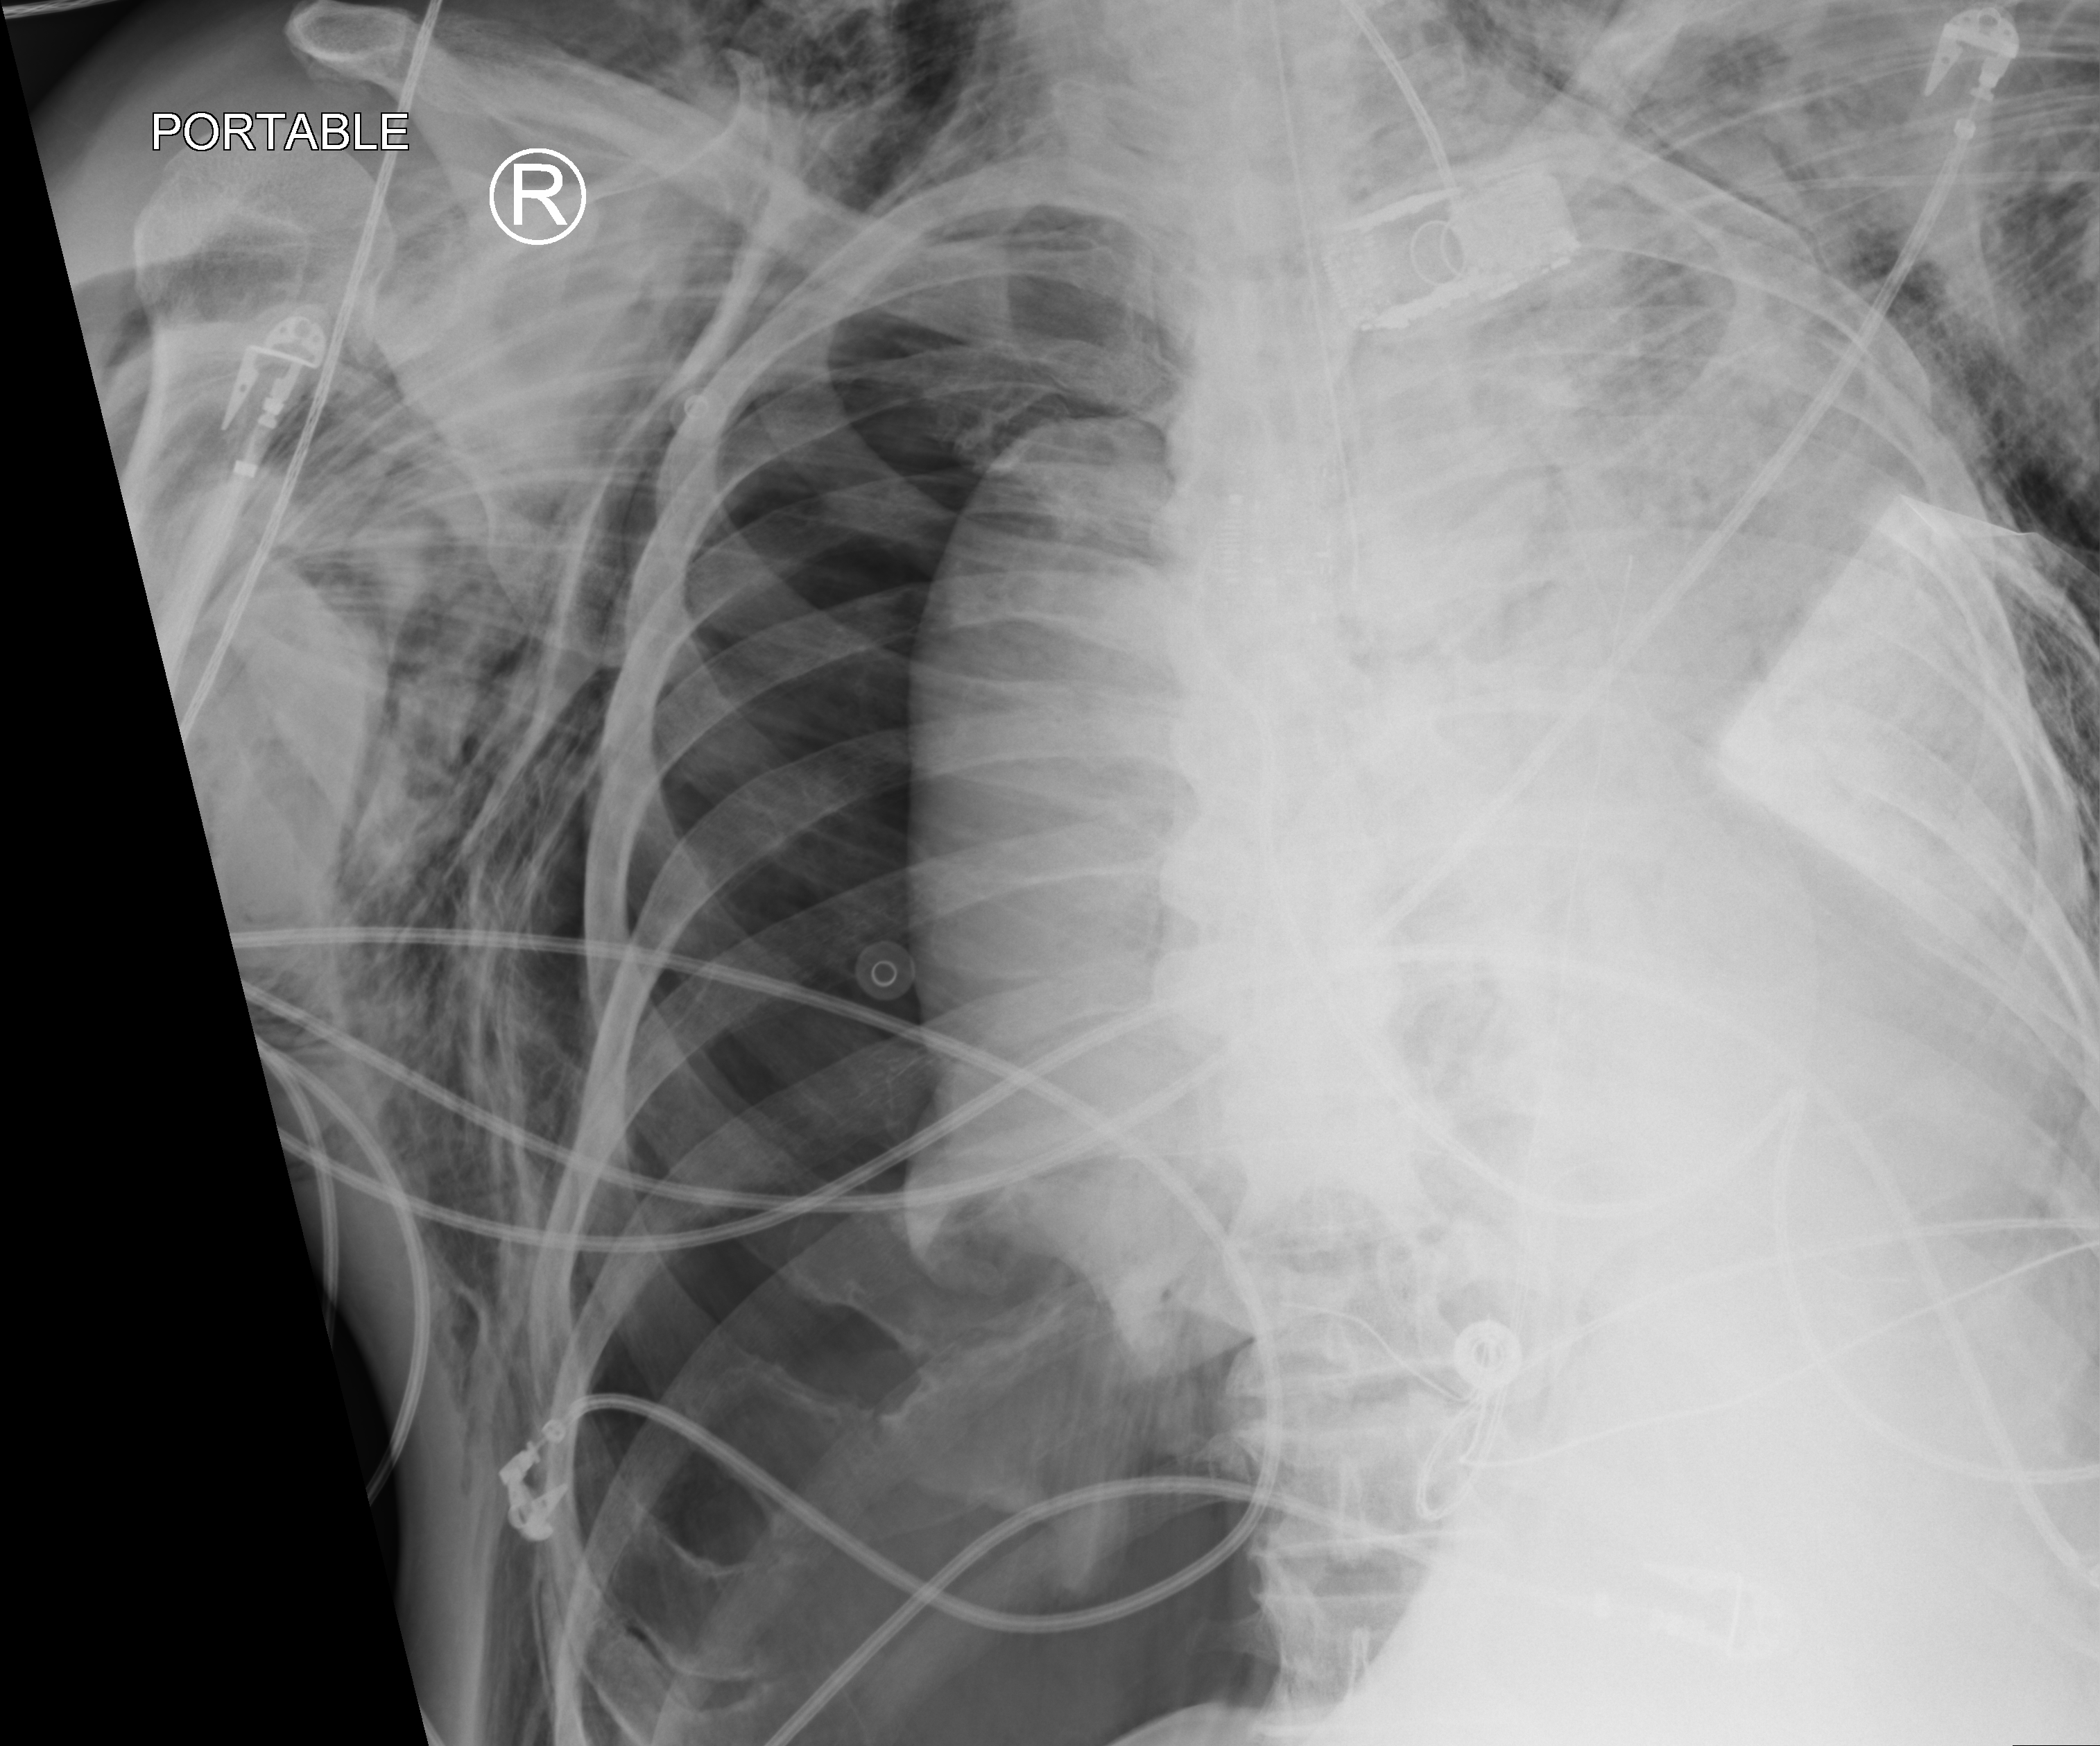
Portable chest radiograph, anteroposterior (AP) projection. Patient hospitalised with COVID-19; male, aged 75–90 years.
From the hospital-stay record, not from the radiograph (when in the stay this image was taken is not recorded):
- COPD (admission record): no
- mechanically ventilated during this hospital stay: yes